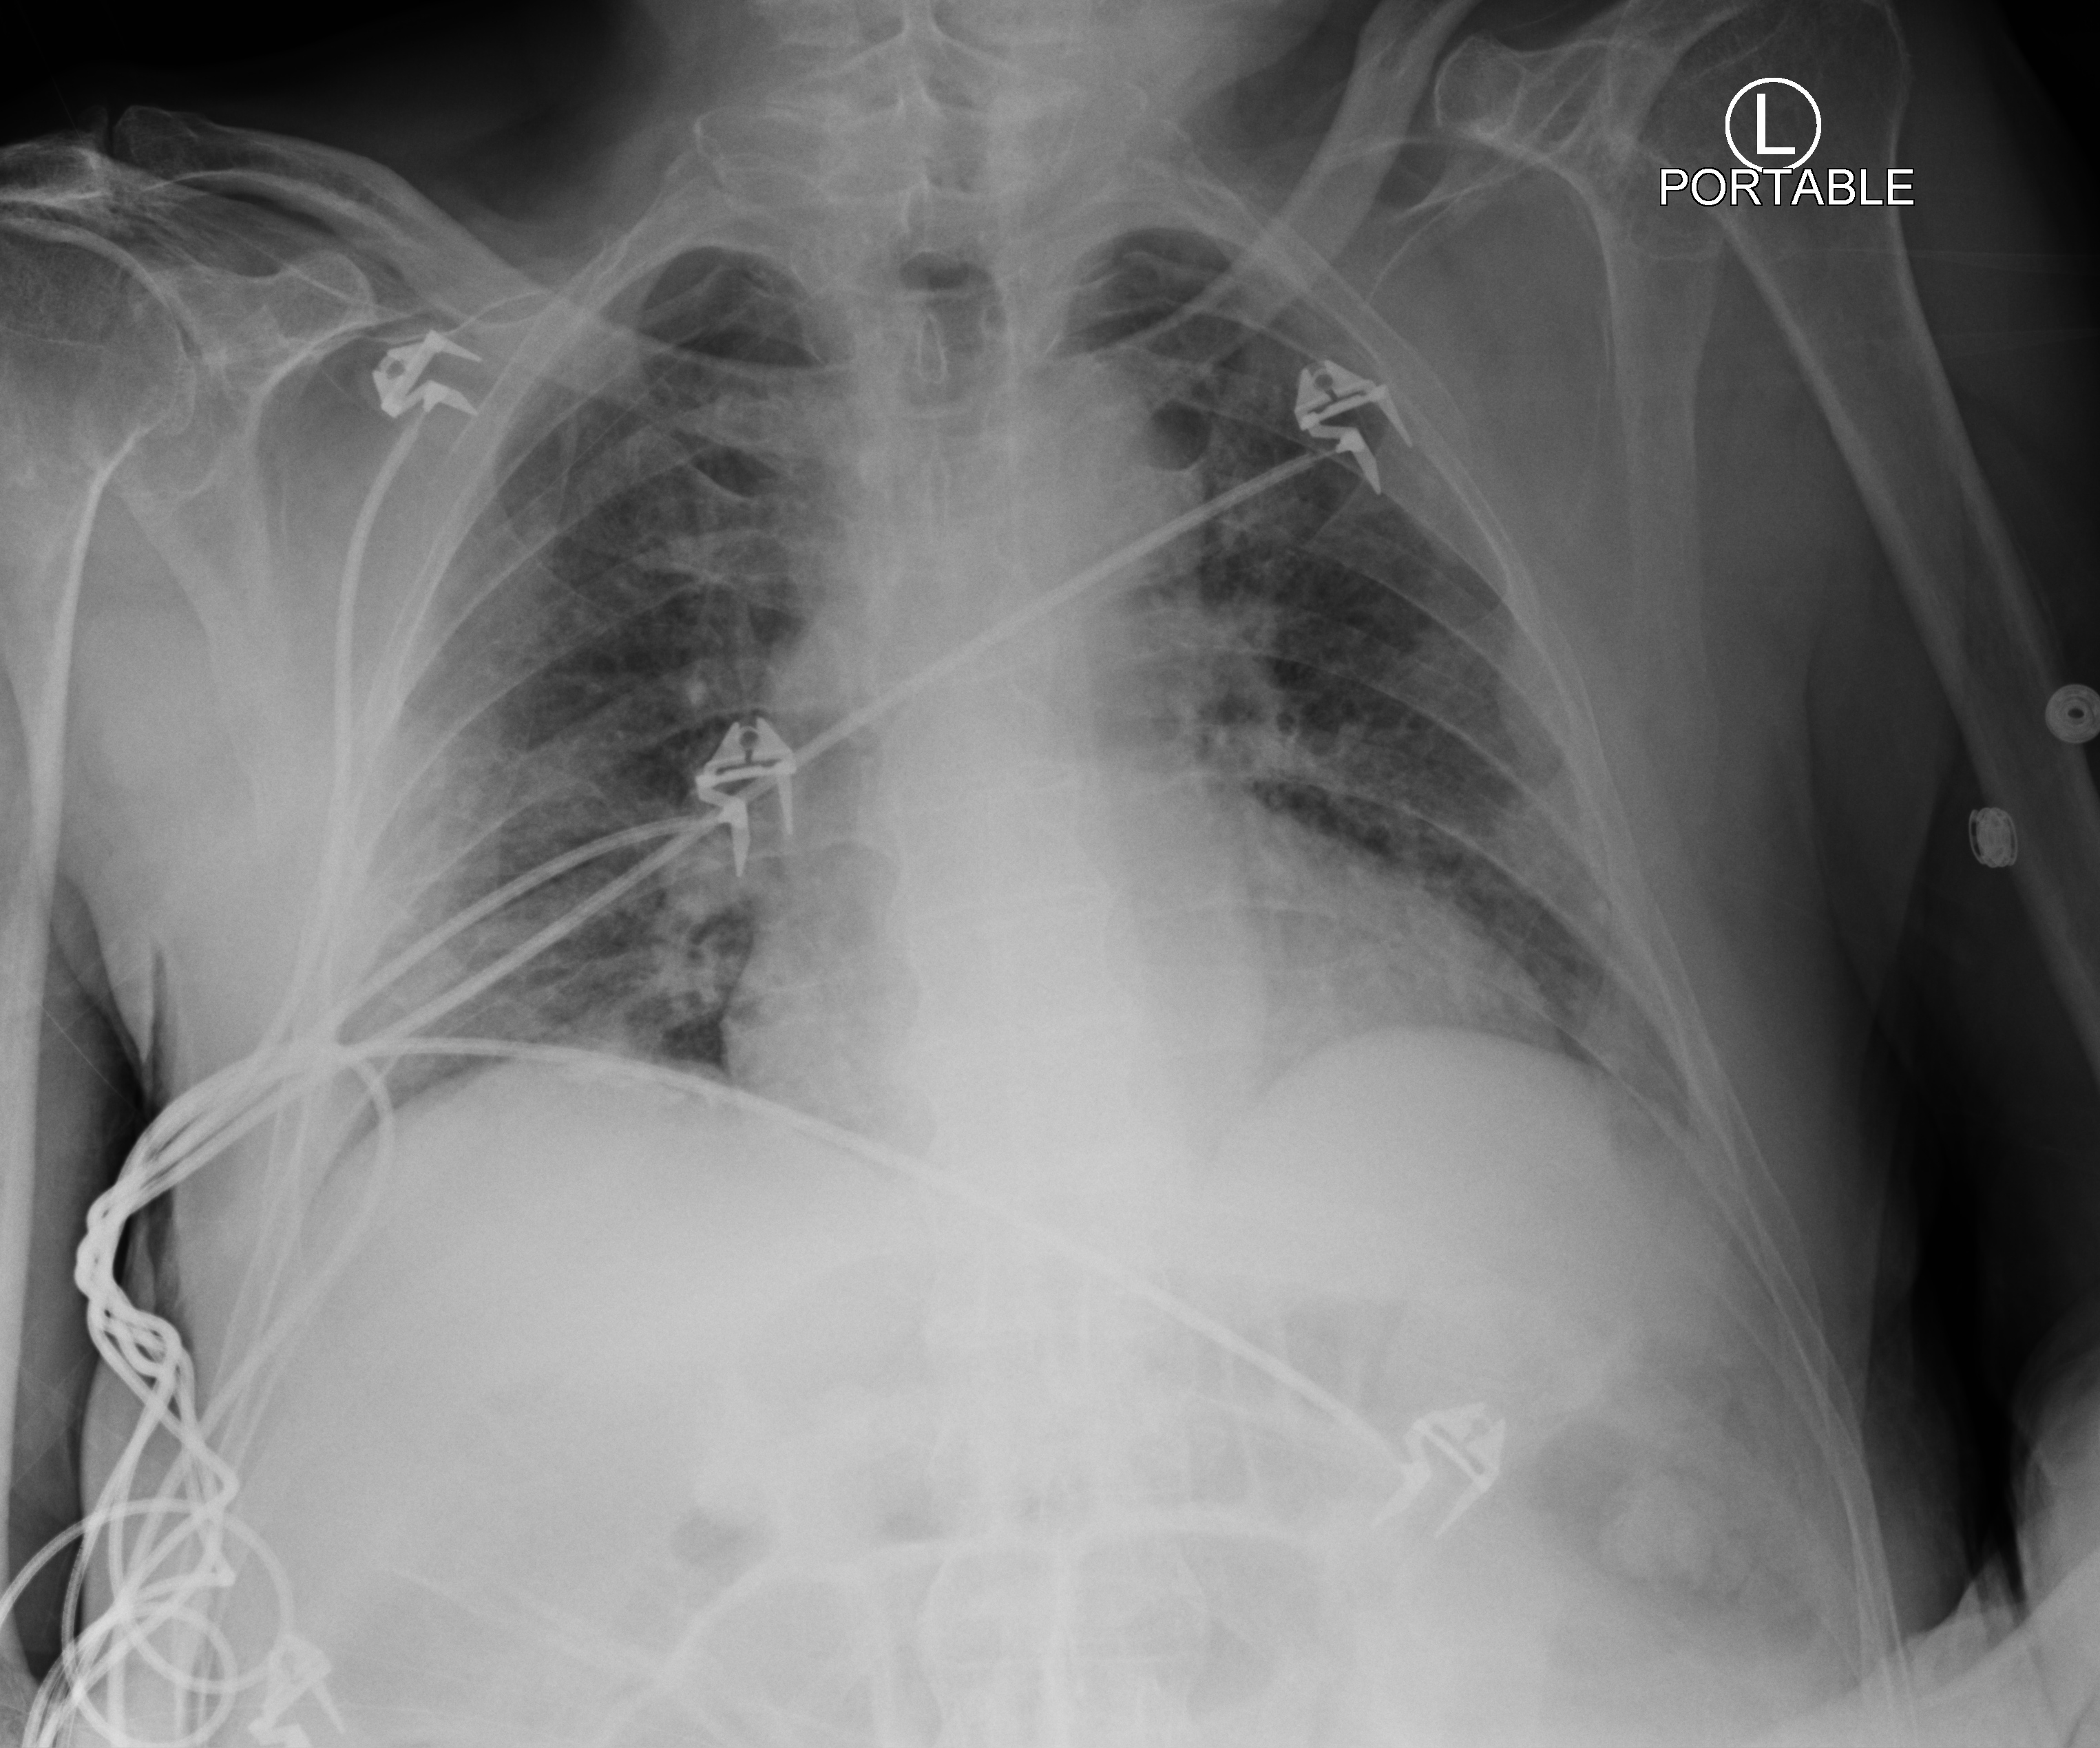
Bedside chest radiograph (computed radiography), anteroposterior (AP) projection. Male patient hospitalised with COVID-19, age 75–90 years.
Admission-level facts for this patient (not findings on this image; timing relative to this image not recorded): mechanically ventilated during this hospital stay: no; admitted to intensive care during this hospital stay: no.